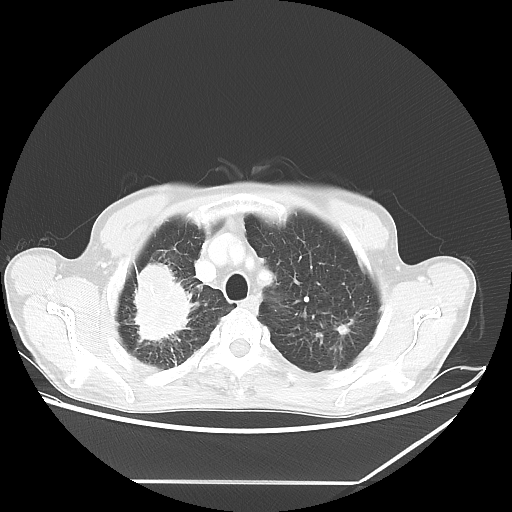
Chest CT, one axial slice; slice 52 of 65 in the series (ordered by position); 80 kVp; lung window (W 1500 / L -600 HU); 512 × 512 image matrix, field of view 397 × 397 mm. Male patient, age 68 years. From the clinical record (not read from this slice): clinical TNM (as recorded): T3 N3 M0.
Structures marked on this image (rectangle marked by the reading radiologist):
- lung tumour (recorded histology: adenocarcinoma): bounding box [x1, y1, x2, y2] px = [125, 254, 189, 359]